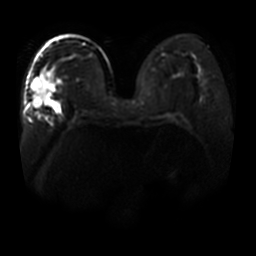
Breast MRI, one axial slice. Slice 24 of 44 in the series (ordered by position). Diffusion-weighted series; image 2 of 4 stored at this slice position (different b-values; order by instance number). 3 T. 5 mm slice thickness. 256 × 256 image matrix. Female patient.
Annotated regions visible in this slice (outlined manually by an expert reader):
- tumour on diffusion-weighted imaging: box from (x=33, y=76) to (x=56, y=107) px